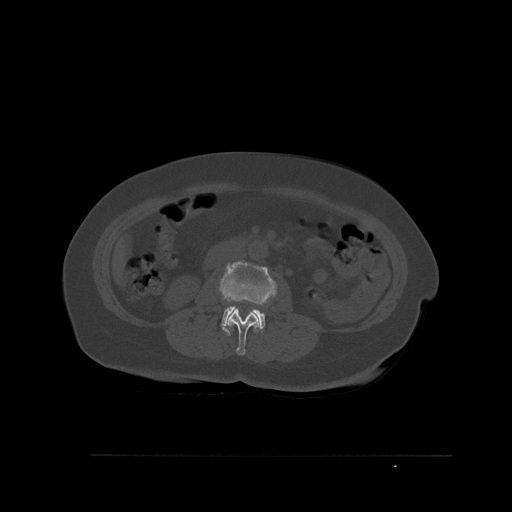
CT including the spine, one axial slice. Position 236 of 527 along the scan axis. Bone window (W 1800 / L 400 HU). 1.5 mm slice thickness. 512 × 512 image matrix. Patient: female, 73 years. From the clinical record (not read from this slice): primary cancer: breast.
Structures marked on this image (semi-automatically segmented with operator editing):
- L2 vertebra: bounding box <227,309,259,355> (left, top, right, bottom; pixels)
- L3 vertebra: <219,260,278,336>
- L4 vertebra: <246,311,260,332>